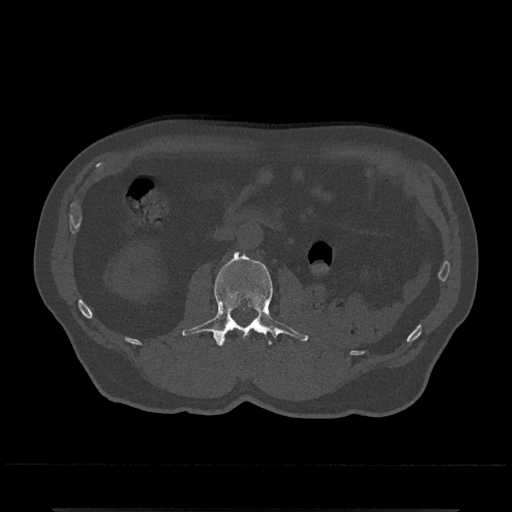
CT including the spine, one axial slice. Position 296 of 797 along the scan axis. Reconstruction kernel Br40s/3. 120 kVp. Bone window (W 1800 / L 400 HU). 0.5 mm slice thickness. 512 × 512 image matrix, field of view 393 × 393 mm. Male patient, age 67 years. From the clinical record (not read from this slice): primary cancer: prostate.
Annotated regions visible in this slice (semi-automatically segmented with operator editing):
- L2 vertebra: bounding box <181,252,309,347> (left, top, right, bottom; pixels)